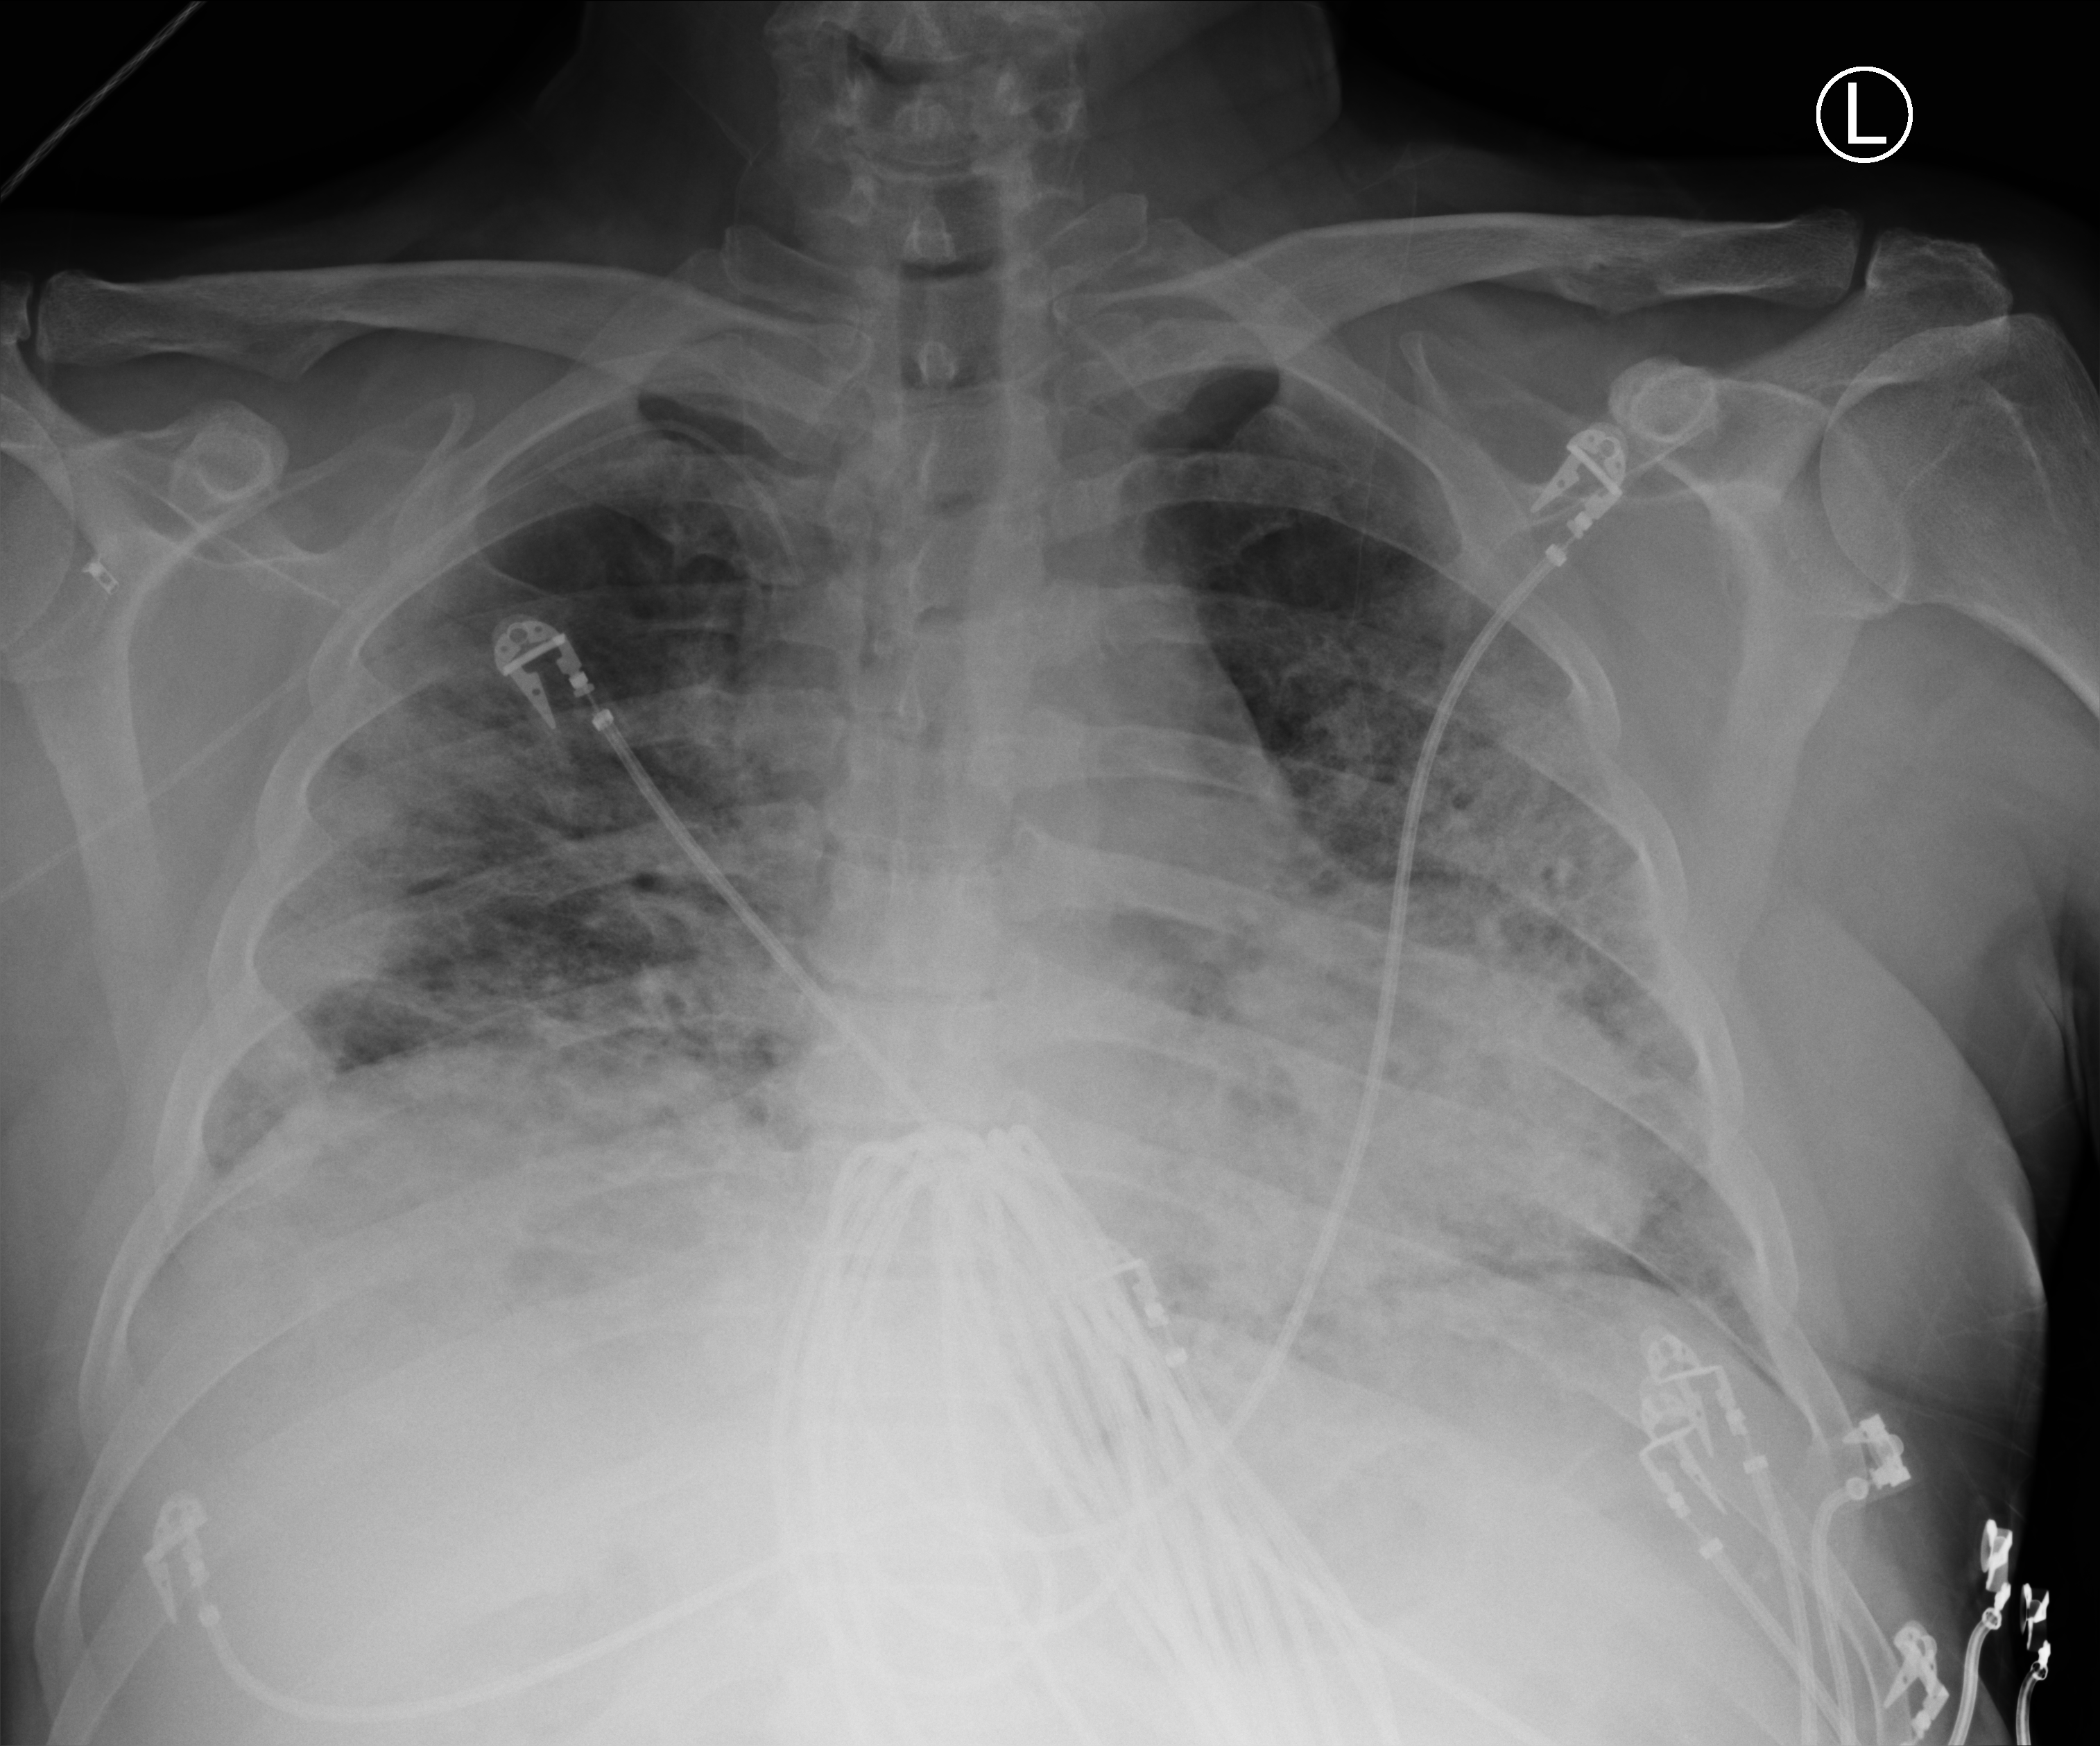
Bedside chest radiograph (computed radiography), anteroposterior (AP) projection. Male patient hospitalised with COVID-19, age 18–59 years.
From the hospital-stay record, not from the radiograph (when in the stay this image was taken is not recorded): admitted to intensive care during this hospital stay: yes; mechanically ventilated during this hospital stay: yes.